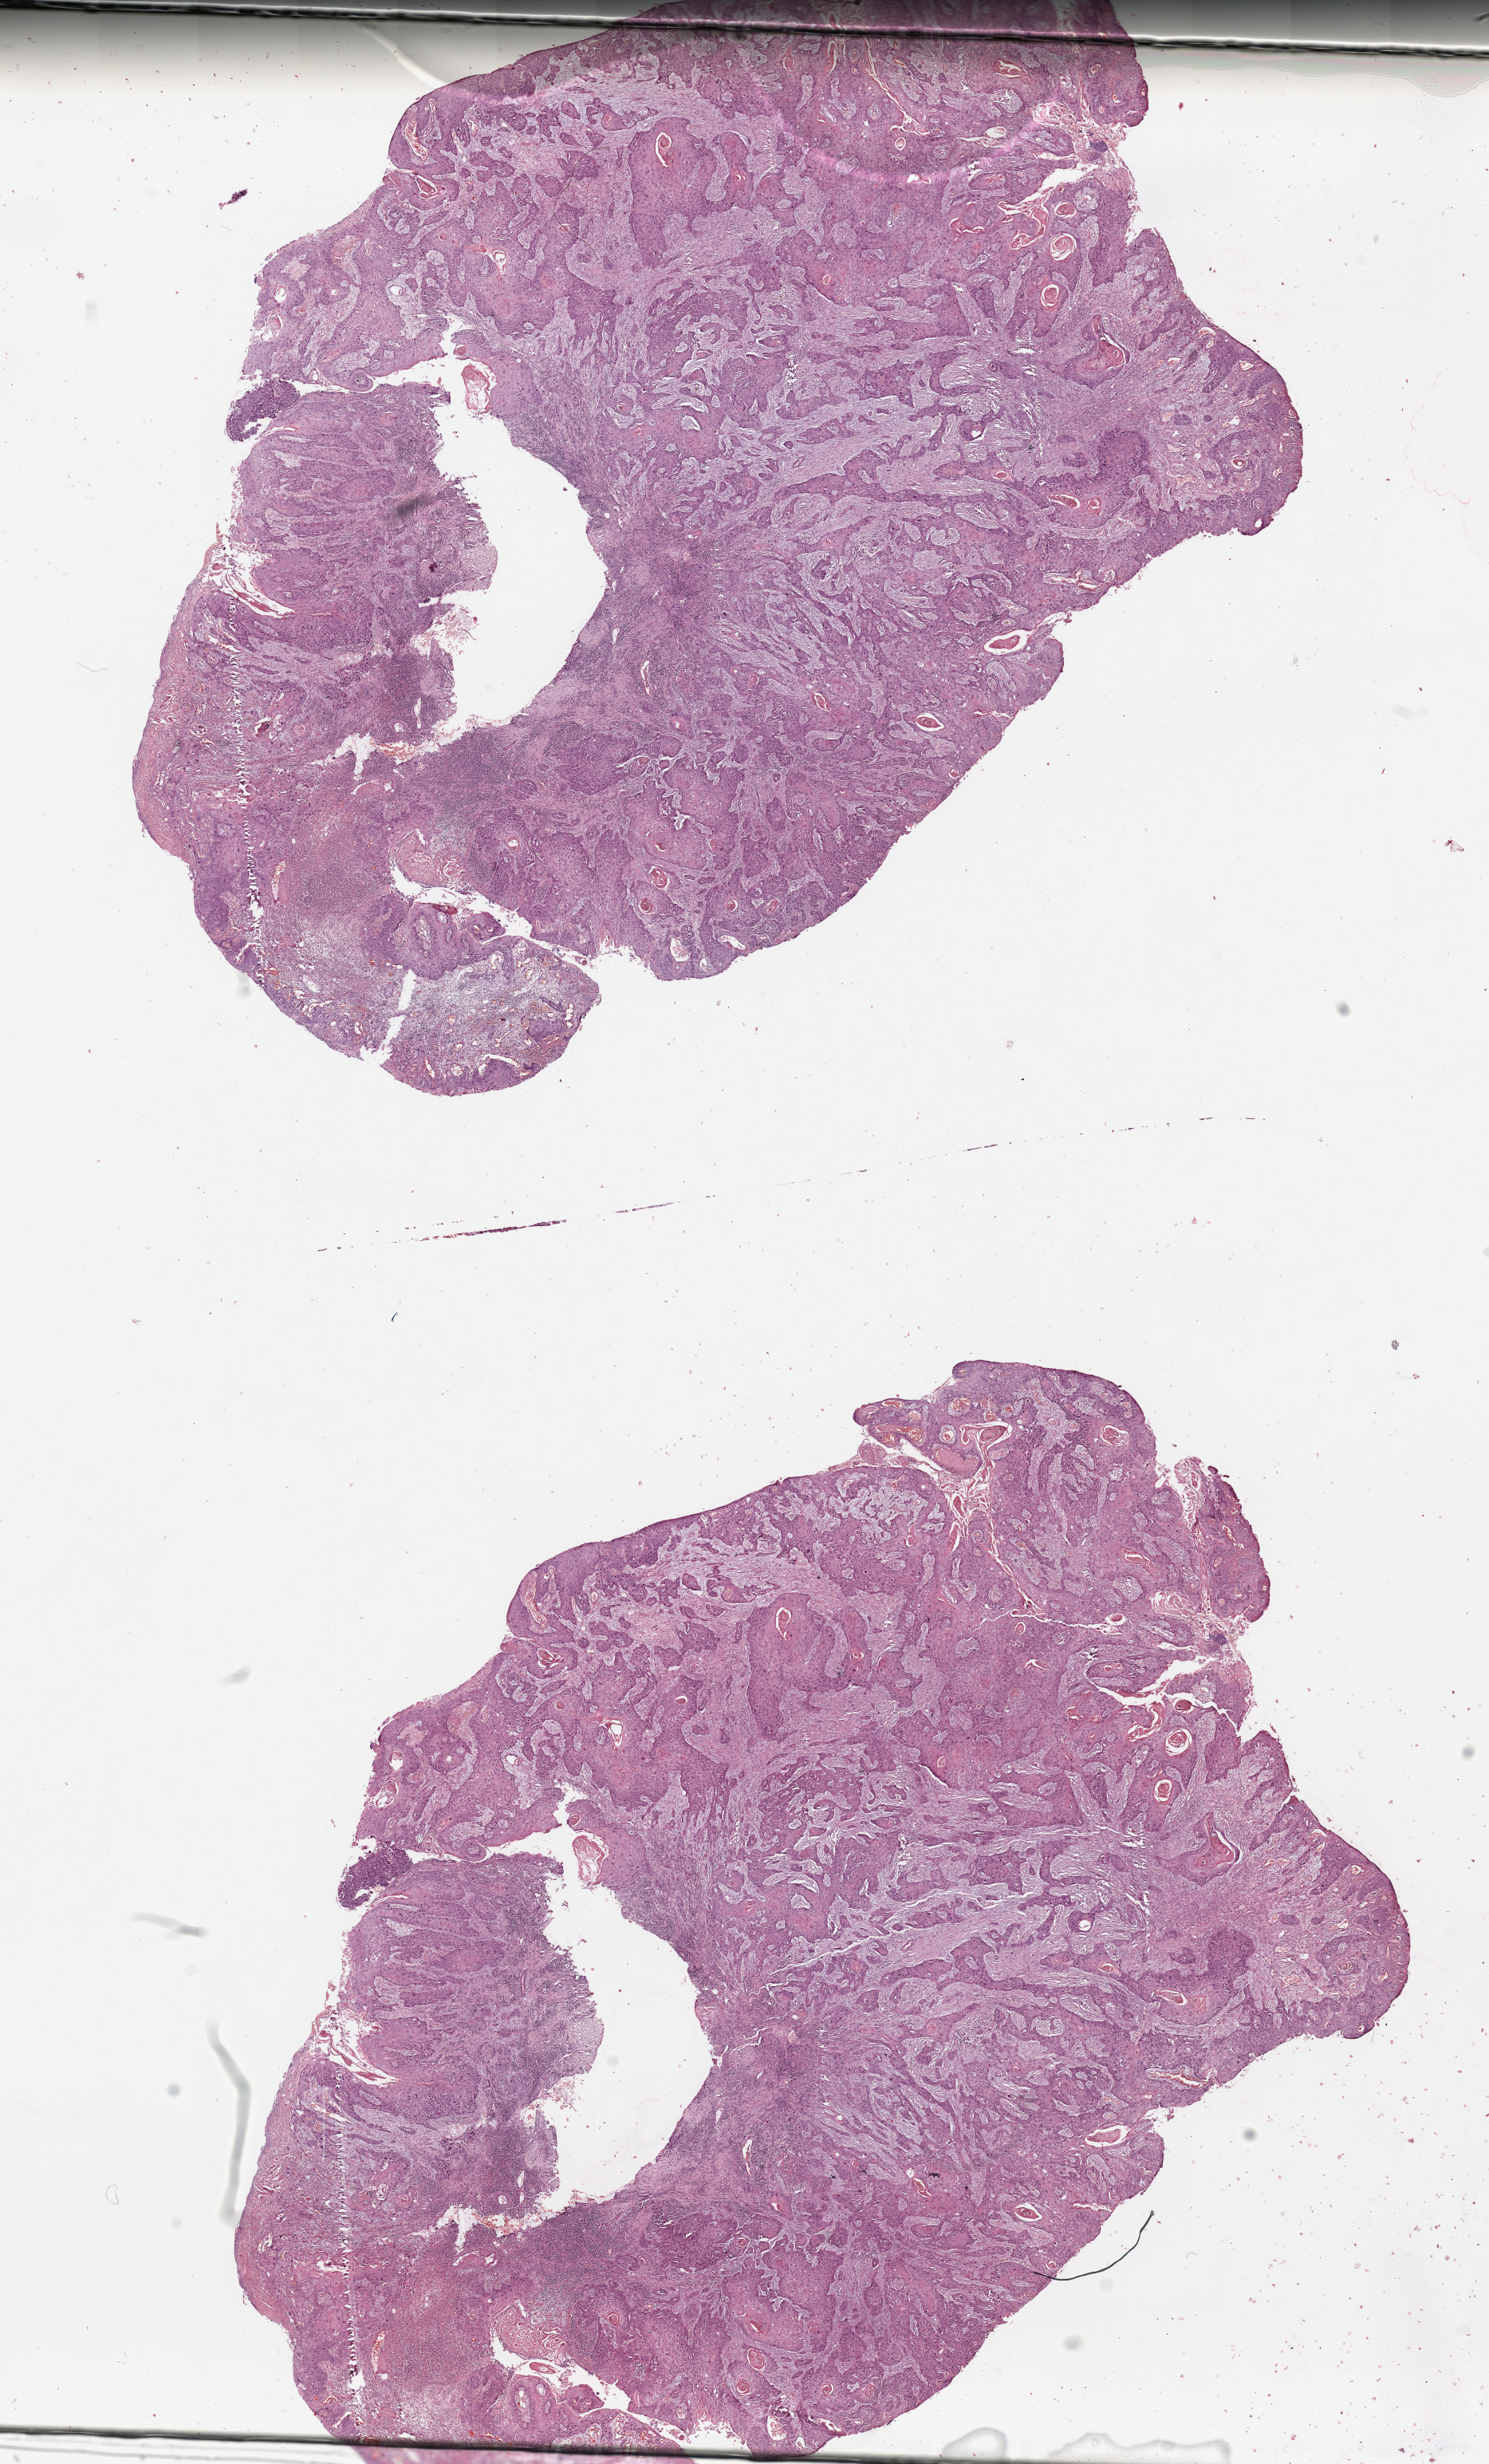
Whole-slide histology image, H&E-stained, low-resolution overview of the scanned area, about 14.8 x 24.4 mm (from a 20x scan), head and neck, tissue type not recorded. Patient: male, age 64 years.
Patient diagnosis: Squamous cell carcinoma, NOS (head, face or neck, NOS).